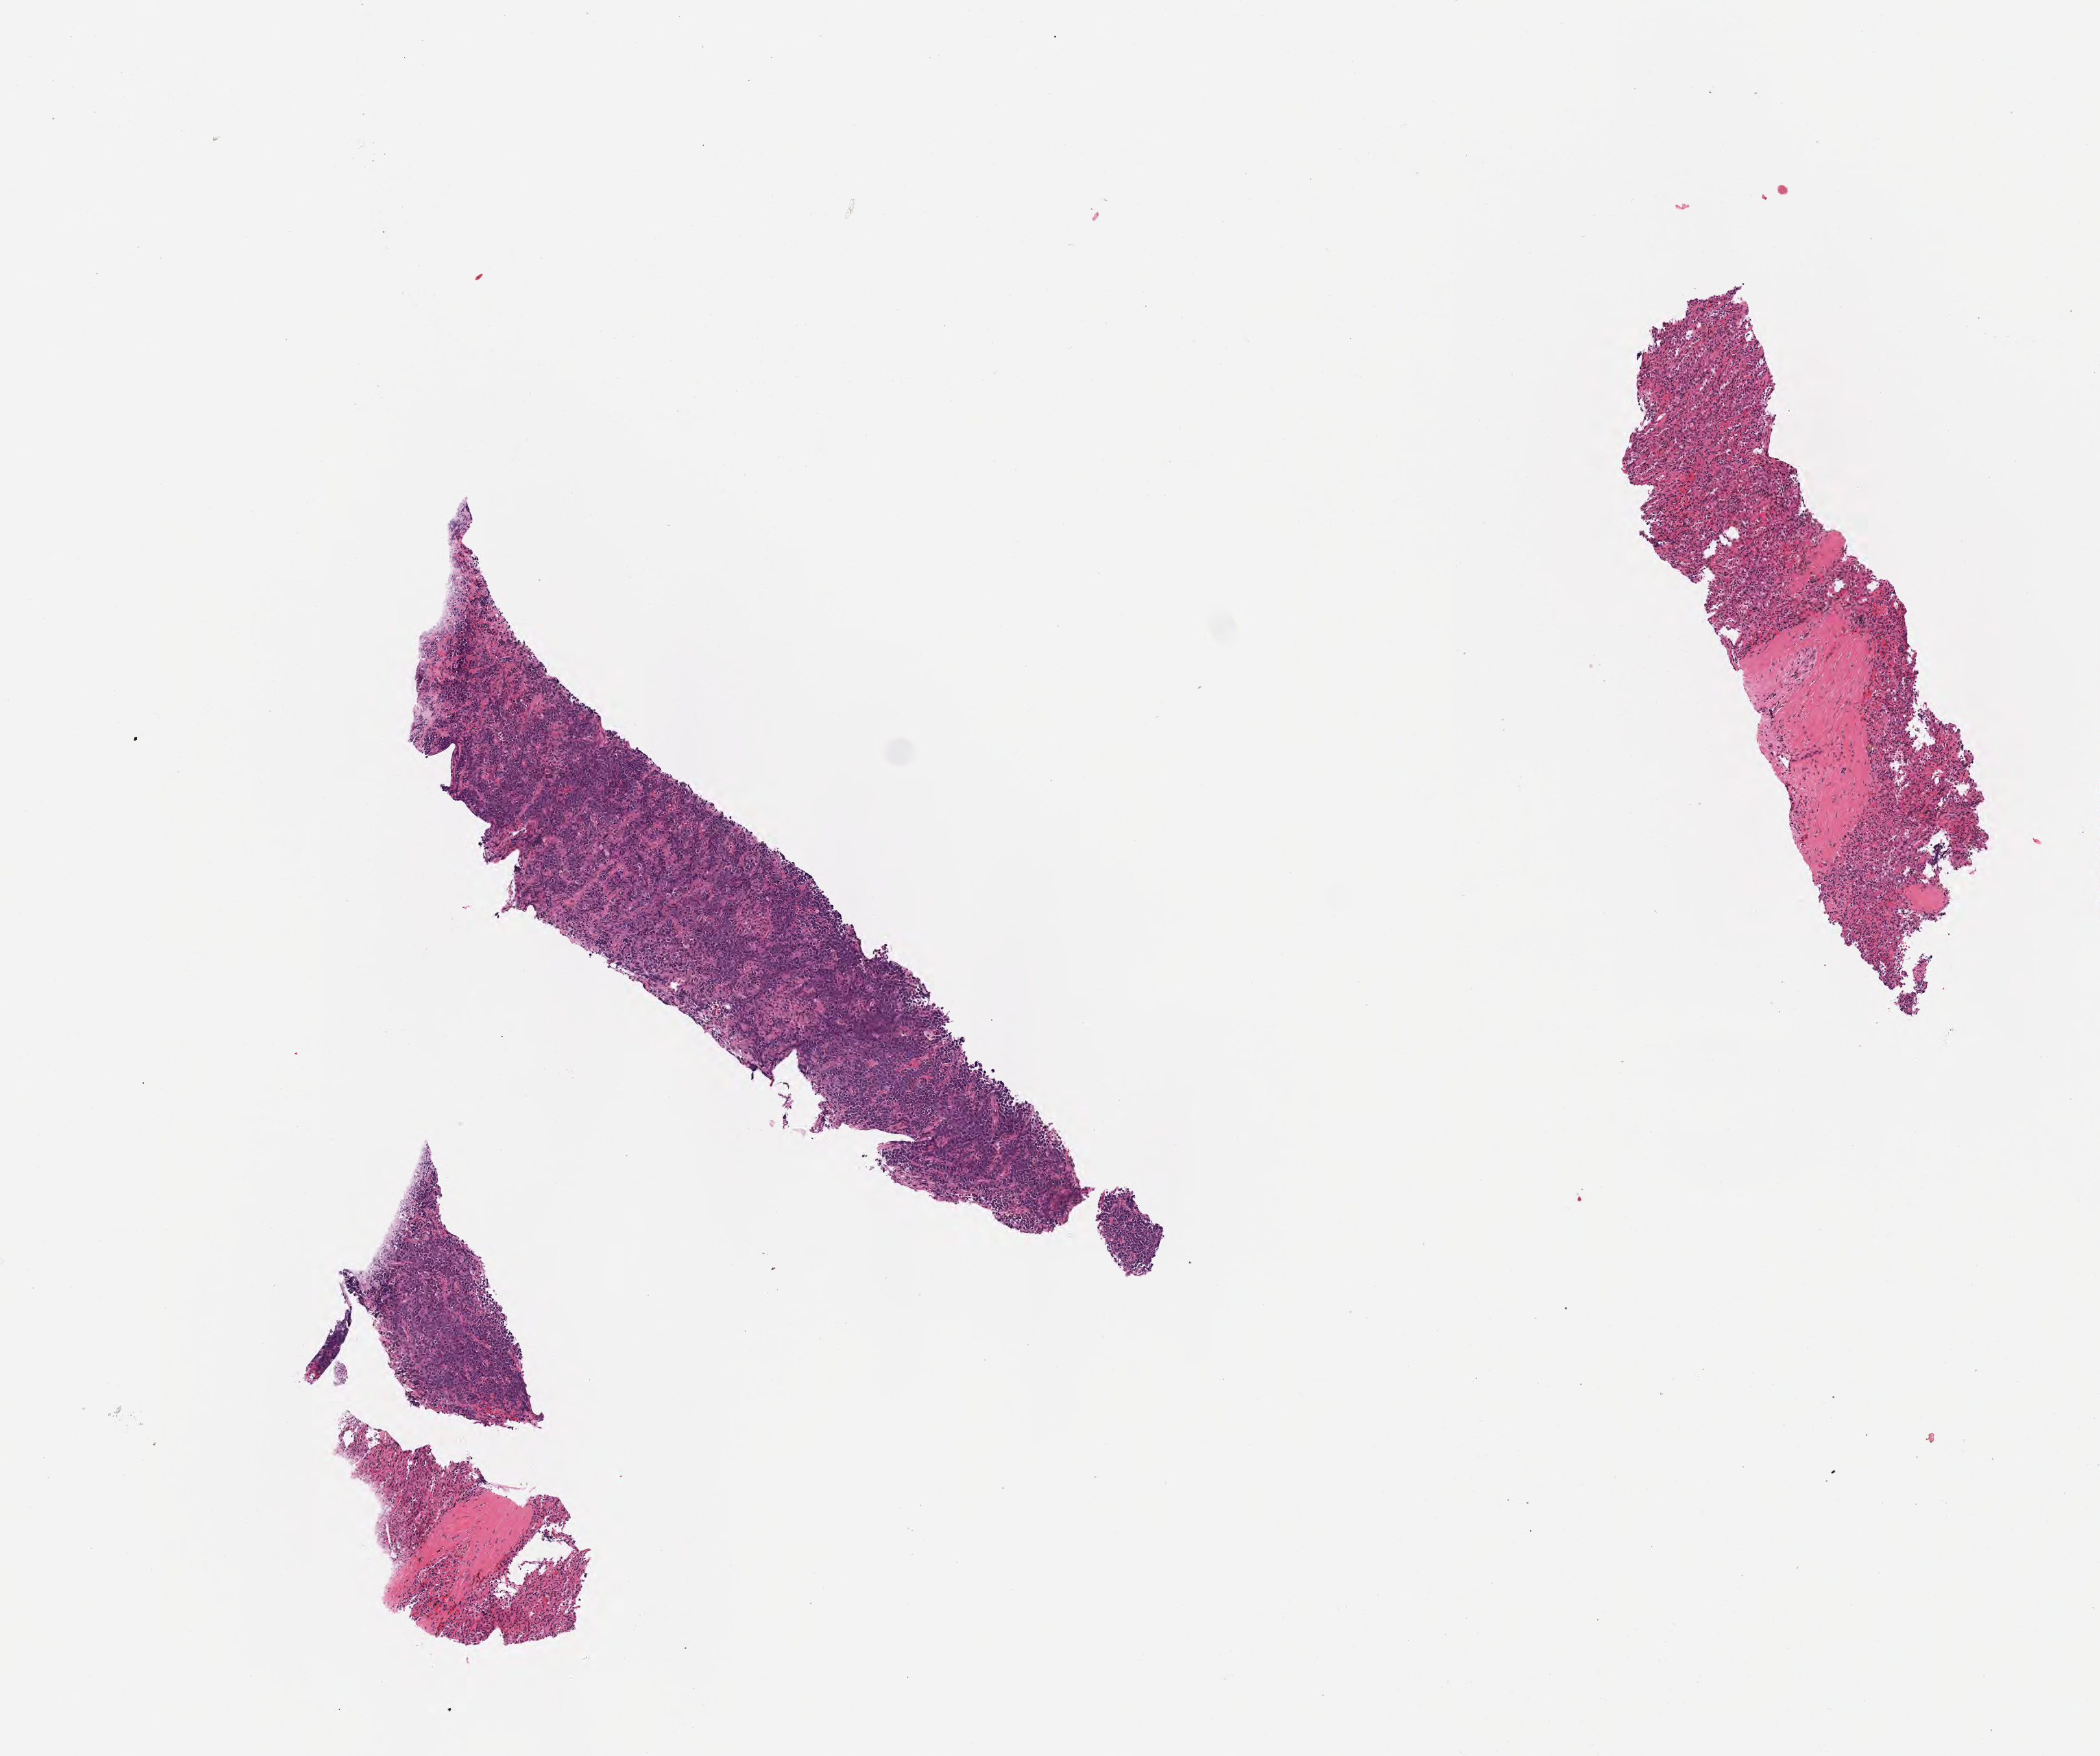
Haematoxylin and eosin whole-slide image, shown as a low-resolution overview of the whole scanned area (about 6.5 x 5.5 mm); specimen: tumor tissue. Patient male; aged 13.
• diagnosis: Diffuse large B-cell lymphoma, NOS